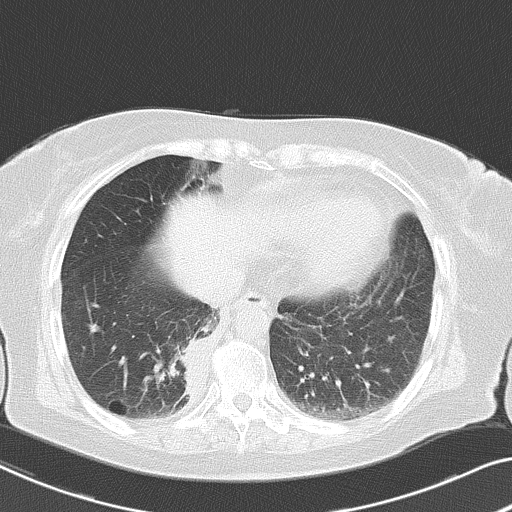
Chest CT, one axial slice. Position 15 of 53 along the scan axis. Reconstruction kernel B70f. 120 kVp. Lung window (W 1500 / L -600 HU). 512 × 512 image matrix. Patient: female, 70 years. Case-level facts recorded for this patient, not image findings: clinical TNM (as recorded): T2 N1 M1a.
Structures marked on this image (rectangle marked by the reading radiologist):
- lung tumour (recorded histology: adenocarcinoma): box from (x=167, y=323) to (x=209, y=409) px